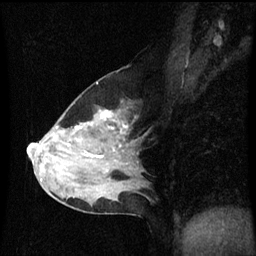
Breast MRI (dynamic contrast-enhanced), one sagittal slice; position 36 of 60 along the scan axis; dynamic contrast-enhanced series, image 2 of 3 at this slice position (ordered by acquisition); 1.5 T; TE 4.2 ms, TR 8.9 ms; 2 mm slice thickness; 256 × 256 image matrix, field of view 200 × 200 mm. Female patient, age 50 years. Case-level facts recorded for this patient, not image findings: setting: breast cancer imaged before/during neoadjuvant chemotherapy; receptor status: HR-positive, HER2-negative.
Annotated regions visible in this slice (semi-automatic segmentation, software-assisted and operator-edited):
- analysis volume of interest (the breast-tissue region the enhancement analysis was run in; not a lesion): box from (x=33, y=92) to (x=138, y=209) px
- tumour enhancement mask (voxels above the 70 % enhancement threshold inside the analysis volume of interest): (x=42, y=110)–(x=114, y=181)